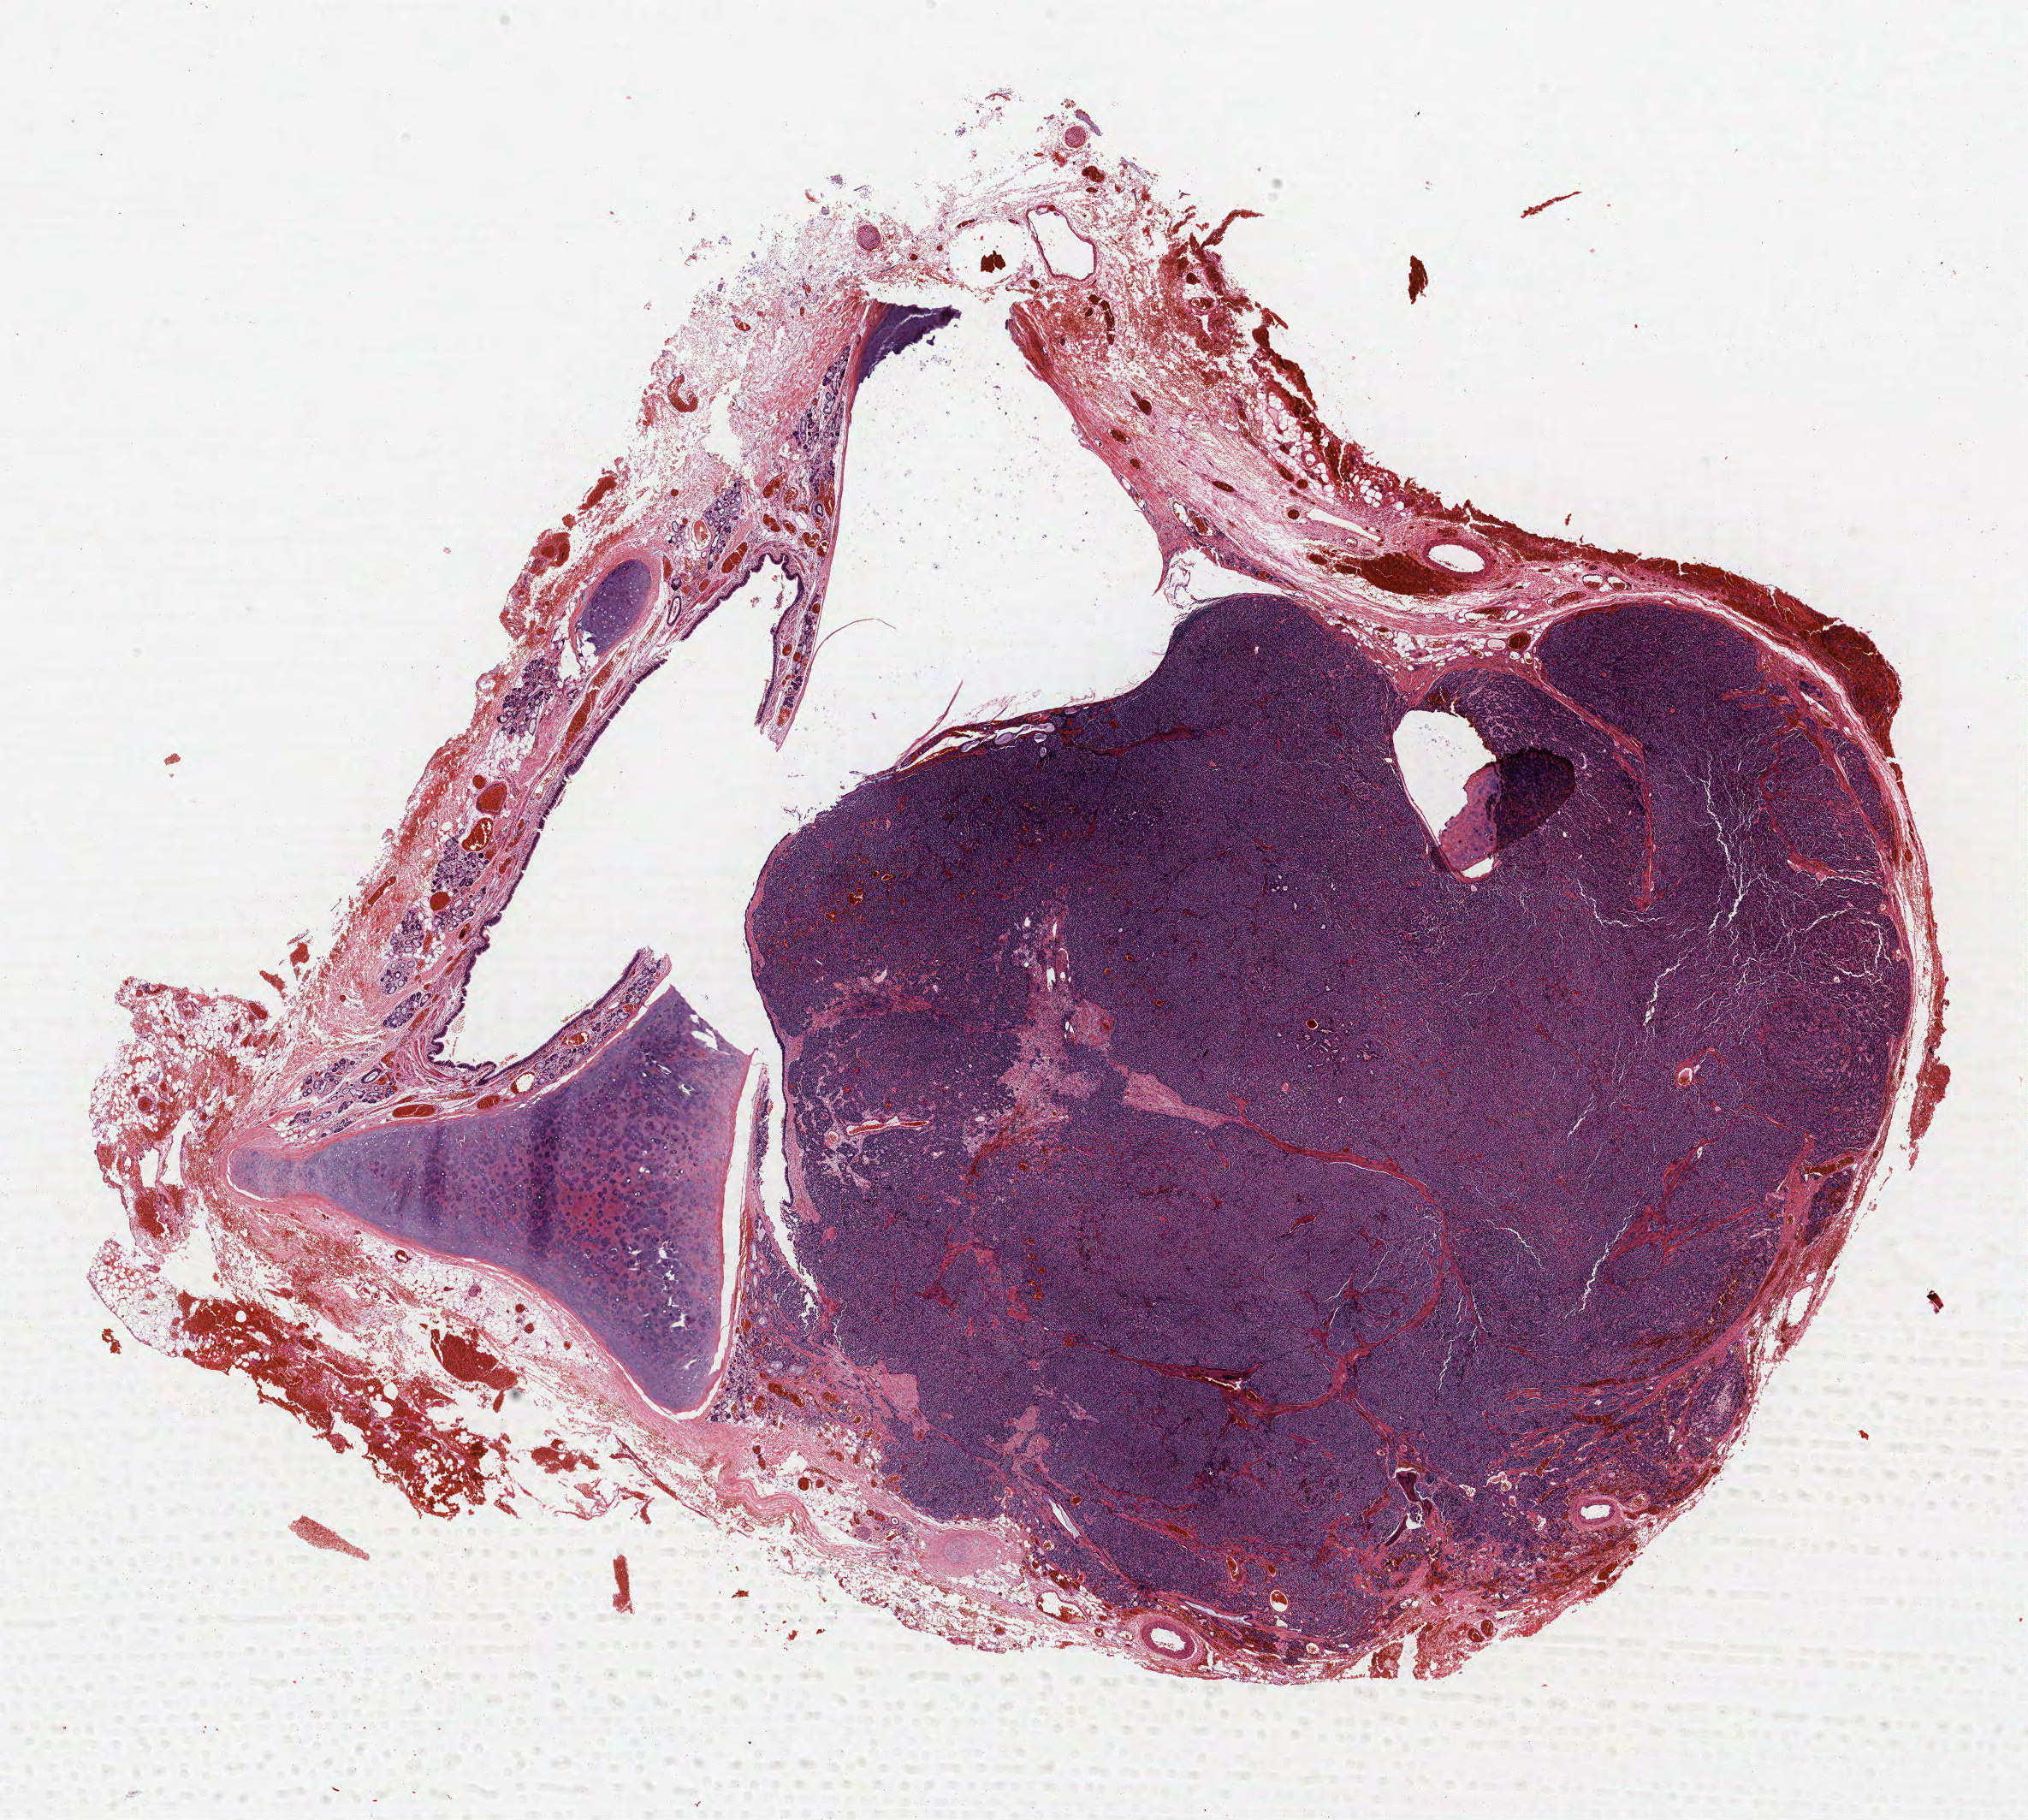
Hematoxylin and eosin (H&E) stained whole-slide image, low-resolution overview of the scanned area, about 19.0 x 17.0 mm; FFPE section; lung. Male patient, aged 57 at enrolment. Former smoker at enrolment.
- primary tumour location (clinical record): right middle lobe
- participant's lung-cancer diagnosis: Carcinoid tumor, NOS
- stage (AJCC 7th edition): IA
- tumour size (pathology): 15 mm